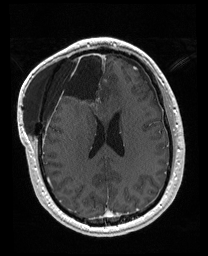
Brain MRI from a brain-tumour surgery series, one axial slice. Slice 73 of 176 in the series (ordered by position). T1-weighted post-contrast. 208 × 256 image matrix, field of view 208 × 256 mm. Case-level facts recorded for this patient, not image findings: histopathology: Astrocytoma; WHO grade: 4; IDH mutation: yes.
Outlined on this slice (outlined manually by an expert reader):
- previous resection cavity: bounding box [x1, y1, x2, y2] px = [56, 52, 106, 111]